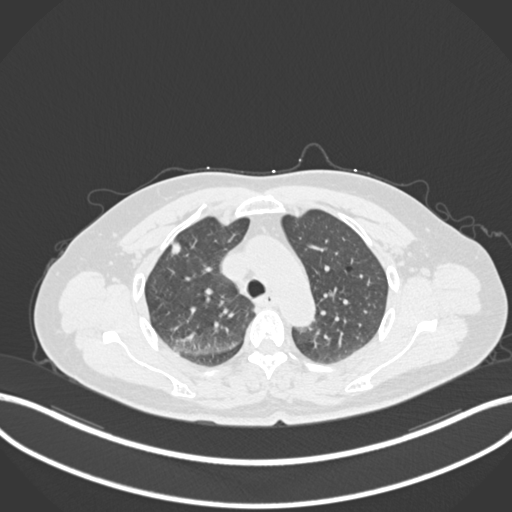
Chest CT, one axial slice. Slice 170 of 223 in the series (ordered by position). Lung window (W 1500 / L -600 HU). 512 × 512 image matrix. Female patient, age 56 years. Case-level facts recorded for this patient, not image findings: clinical TNM (as recorded): T1c N0 M0.
Outlined on this slice (rectangle marked by the reading radiologist):
- lung tumour (recorded histology: adenocarcinoma): box from (x=168, y=241) to (x=185, y=256) px